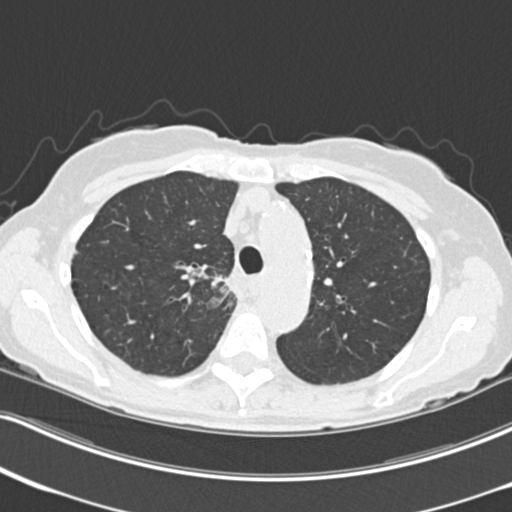
Chest CT (low-dose screening protocol), one axial image. Third annual screen. Lung window (W 1500 / L -600 HU). 2 mm slice thickness. Female, age 68 years at enrolment. Current smoker at enrolment.
Lesion marked by an expert reader, bounding box [x1, y1, x2, y2] px = [194, 268, 249, 325]. Reader record for this screening exam (exam-level; its link to the box is not recorded): non-calcified nodule or mass ≥4 mm, right upper lobe, 31 × 29 mm, poorly defined margins, soft tissue attenuation, pre-existing on the prior screen: no. Official screen result: positive, other.